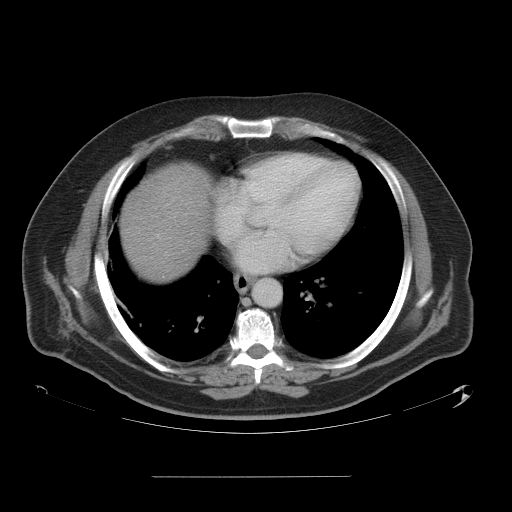
Contrast-enhanced abdominal CT, one axial slice. Position 54 of 58 along the scan axis. 120 kVp. Soft-tissue window (W 400 / L 40 HU). 5 mm slice thickness. 512 × 512 image matrix. Male patient, age 63 years. Case-level facts recorded for this patient, not image findings: diagnosis: colorectal cancer liver metastases, imaged before liver resection; multiple liver metastases: no; largest metastasis: 4.2 cm; disease in both lobes: no.
Annotated regions visible in this slice (manually delineated by an expert):
- hepatic veins: box from (x=218, y=204) to (x=245, y=272) px
- liver: (x=120, y=164)–(x=209, y=282)
- planned liver remnant (the part of the liver to remain after resection): (x=120, y=220)–(x=201, y=282)